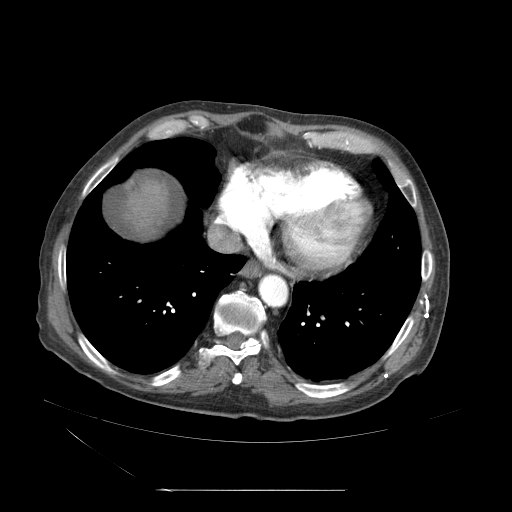
Contrast-enhanced abdominal CT (liver protocol), one axial slice; slice 59 of 71 in the series (ordered by position); reconstruction kernel STANDARD; soft-tissue window (W 400 / L 40 HU); 2.5 mm slice thickness; 512 × 512 image matrix, field of view 440 × 440 mm. From the clinical record (not read from this slice): diagnosis: hepatocellular carcinoma (patient treated with transarterial chemoembolisation; whether this scan precedes or follows treatment is not stated here); TNM stage (as recorded): Stage-II; Child-Pugh class: A.
Outlined on this slice (semi-automatic segmentation, software-assisted and operator-edited):
- abdominal aorta: bounding box <259,272,288,309> (left, top, right, bottom; pixels)
- liver parenchyma outside the tumour (the mass and vessels are separate outlines, so this box may not span the whole liver): <139,172,190,243>